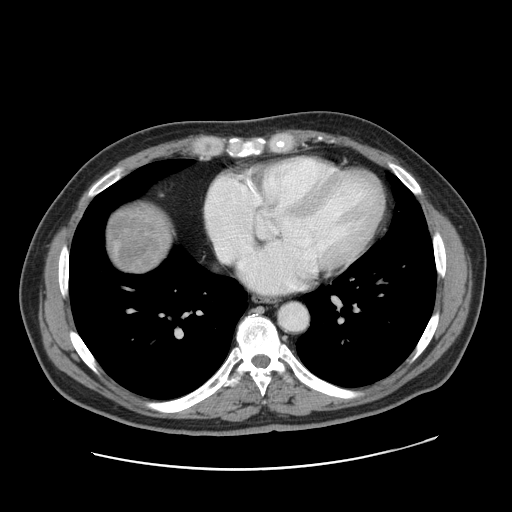
Contrast-enhanced abdominal CT, one axial slice. Slice 164 of 178 in the series (ordered by position). Intravenous contrast given. Soft-tissue window (W 400 / L 40 HU). 2.5 mm slice thickness. 512 × 512 image matrix, field of view 403 × 403 mm. Male patient, age 63 years. Case-level facts recorded for this patient, not image findings: diagnosis: colorectal cancer liver metastases, imaged before liver resection; multiple liver metastases: yes; largest metastasis: 8 cm; chemotherapy before resection: no.
Structures marked on this image (outlined manually by an expert reader):
- liver: box from (x=106, y=206) to (x=170, y=272) px
- liver metastasis: (x=110, y=209)–(x=164, y=272)